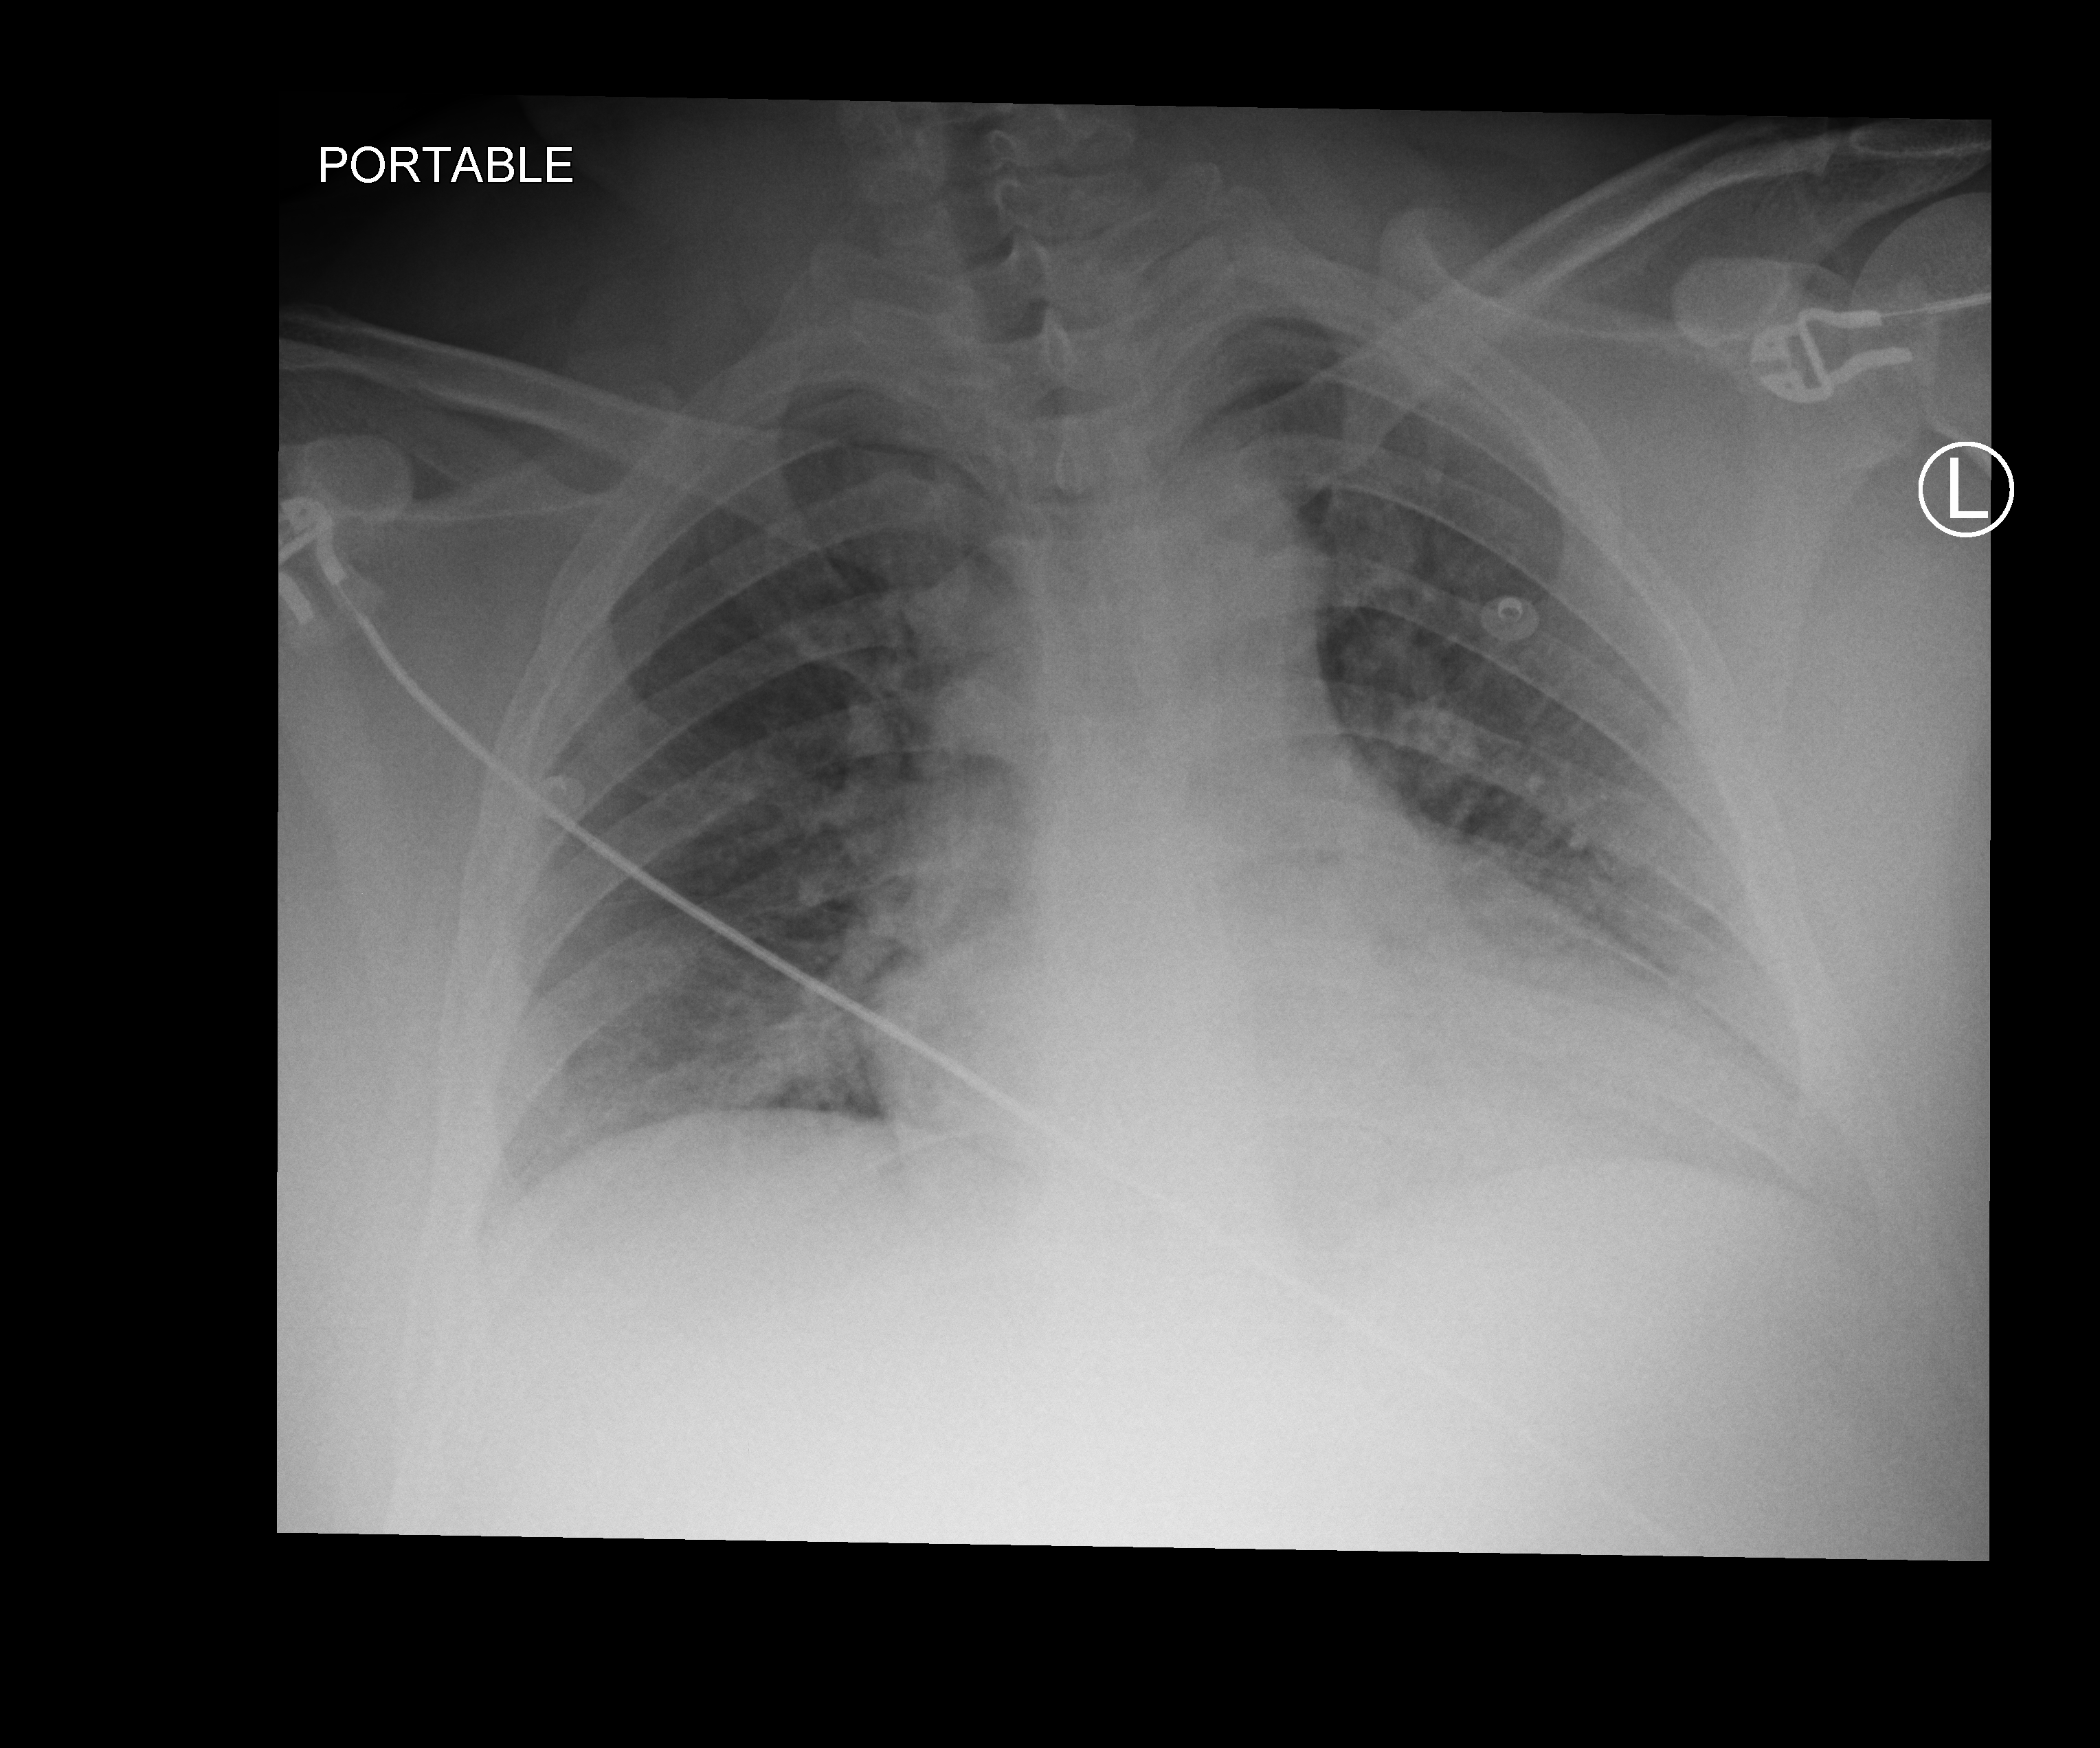
Bedside chest radiograph (computed radiography). Male patient hospitalised with COVID-19, age 18–59 years.
Hospital-stay facts (about this admission, not read from this image; timing relative to this image not recorded):
- admitted to intensive care during this hospital stay: no
- mechanically ventilated during this hospital stay: no